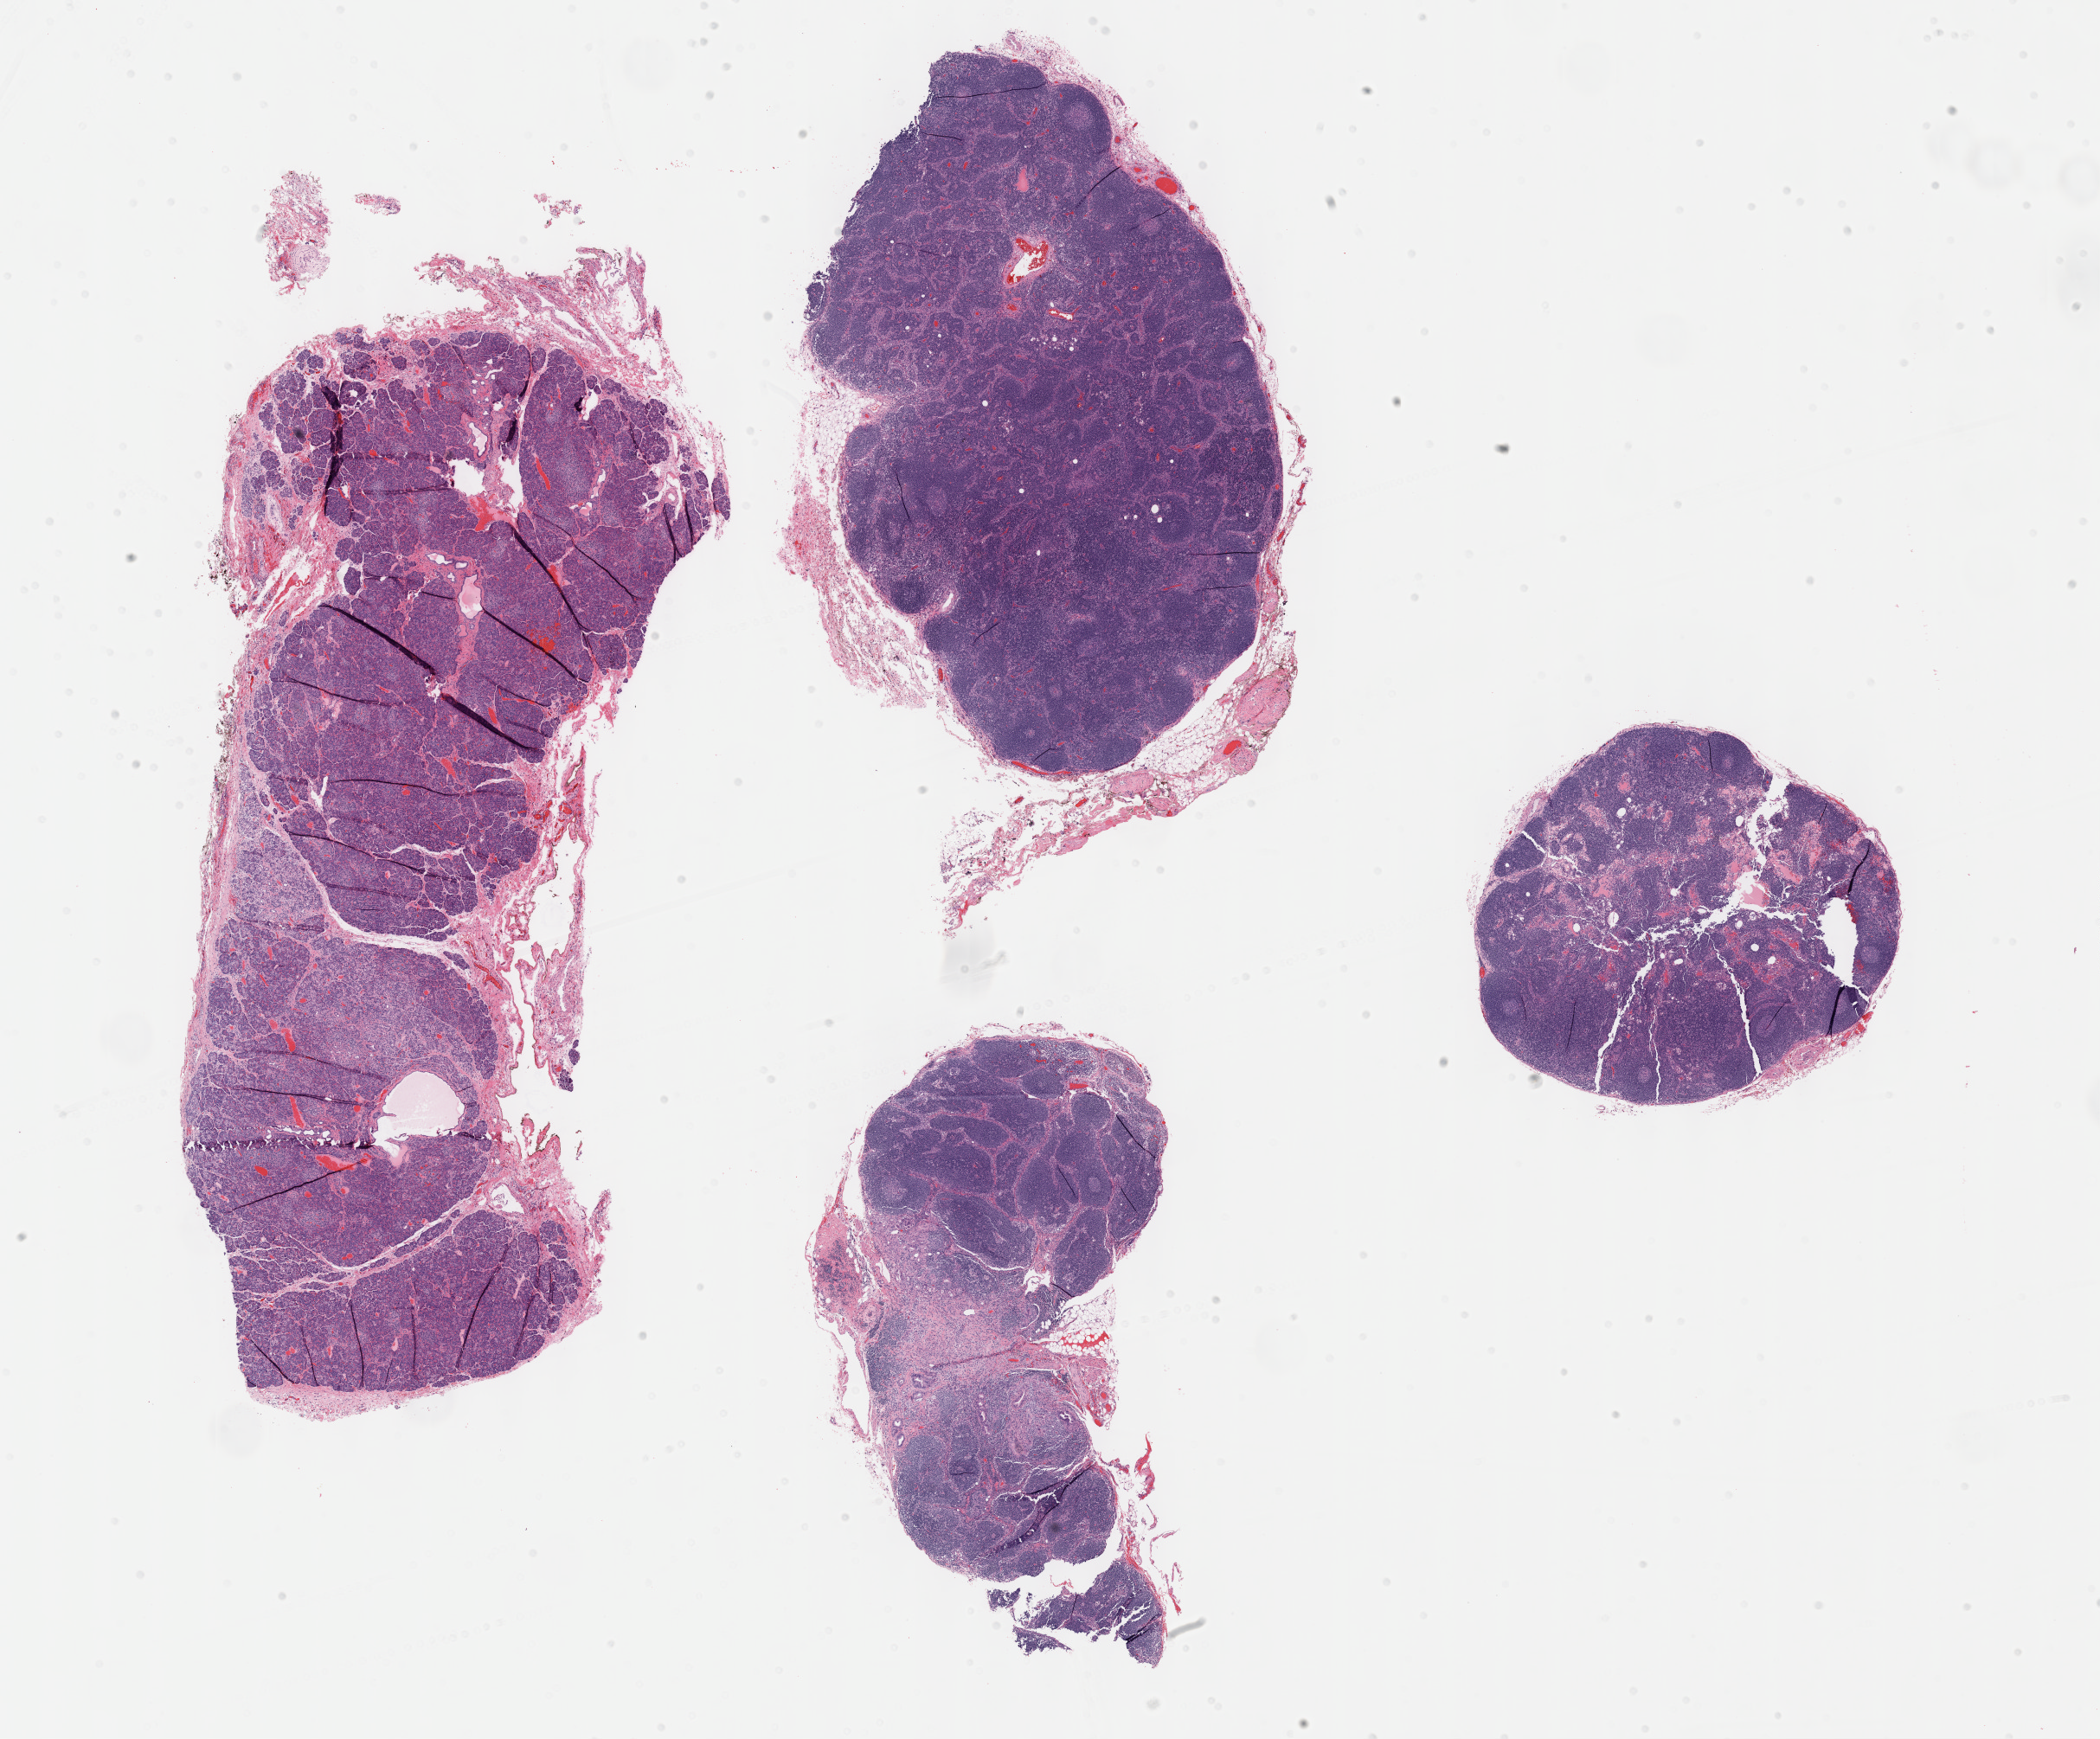
Digitized H&E tissue section (whole slide) — whole scanned area (about 19.6 x 16.3 mm, from a 40x scan) shown as a low-resolution overview. Formalin-fixed paraffin-embedded (FFPE) diagnostic section. Pancreas, primary tumour sample. Female, age 57 years at initial diagnosis. Histologic grade: G2 (moderately differentiated).
Diagnosis: Infiltrating duct carcinoma, NOS (head of pancreas). AJCC pathologic stage: IIB.